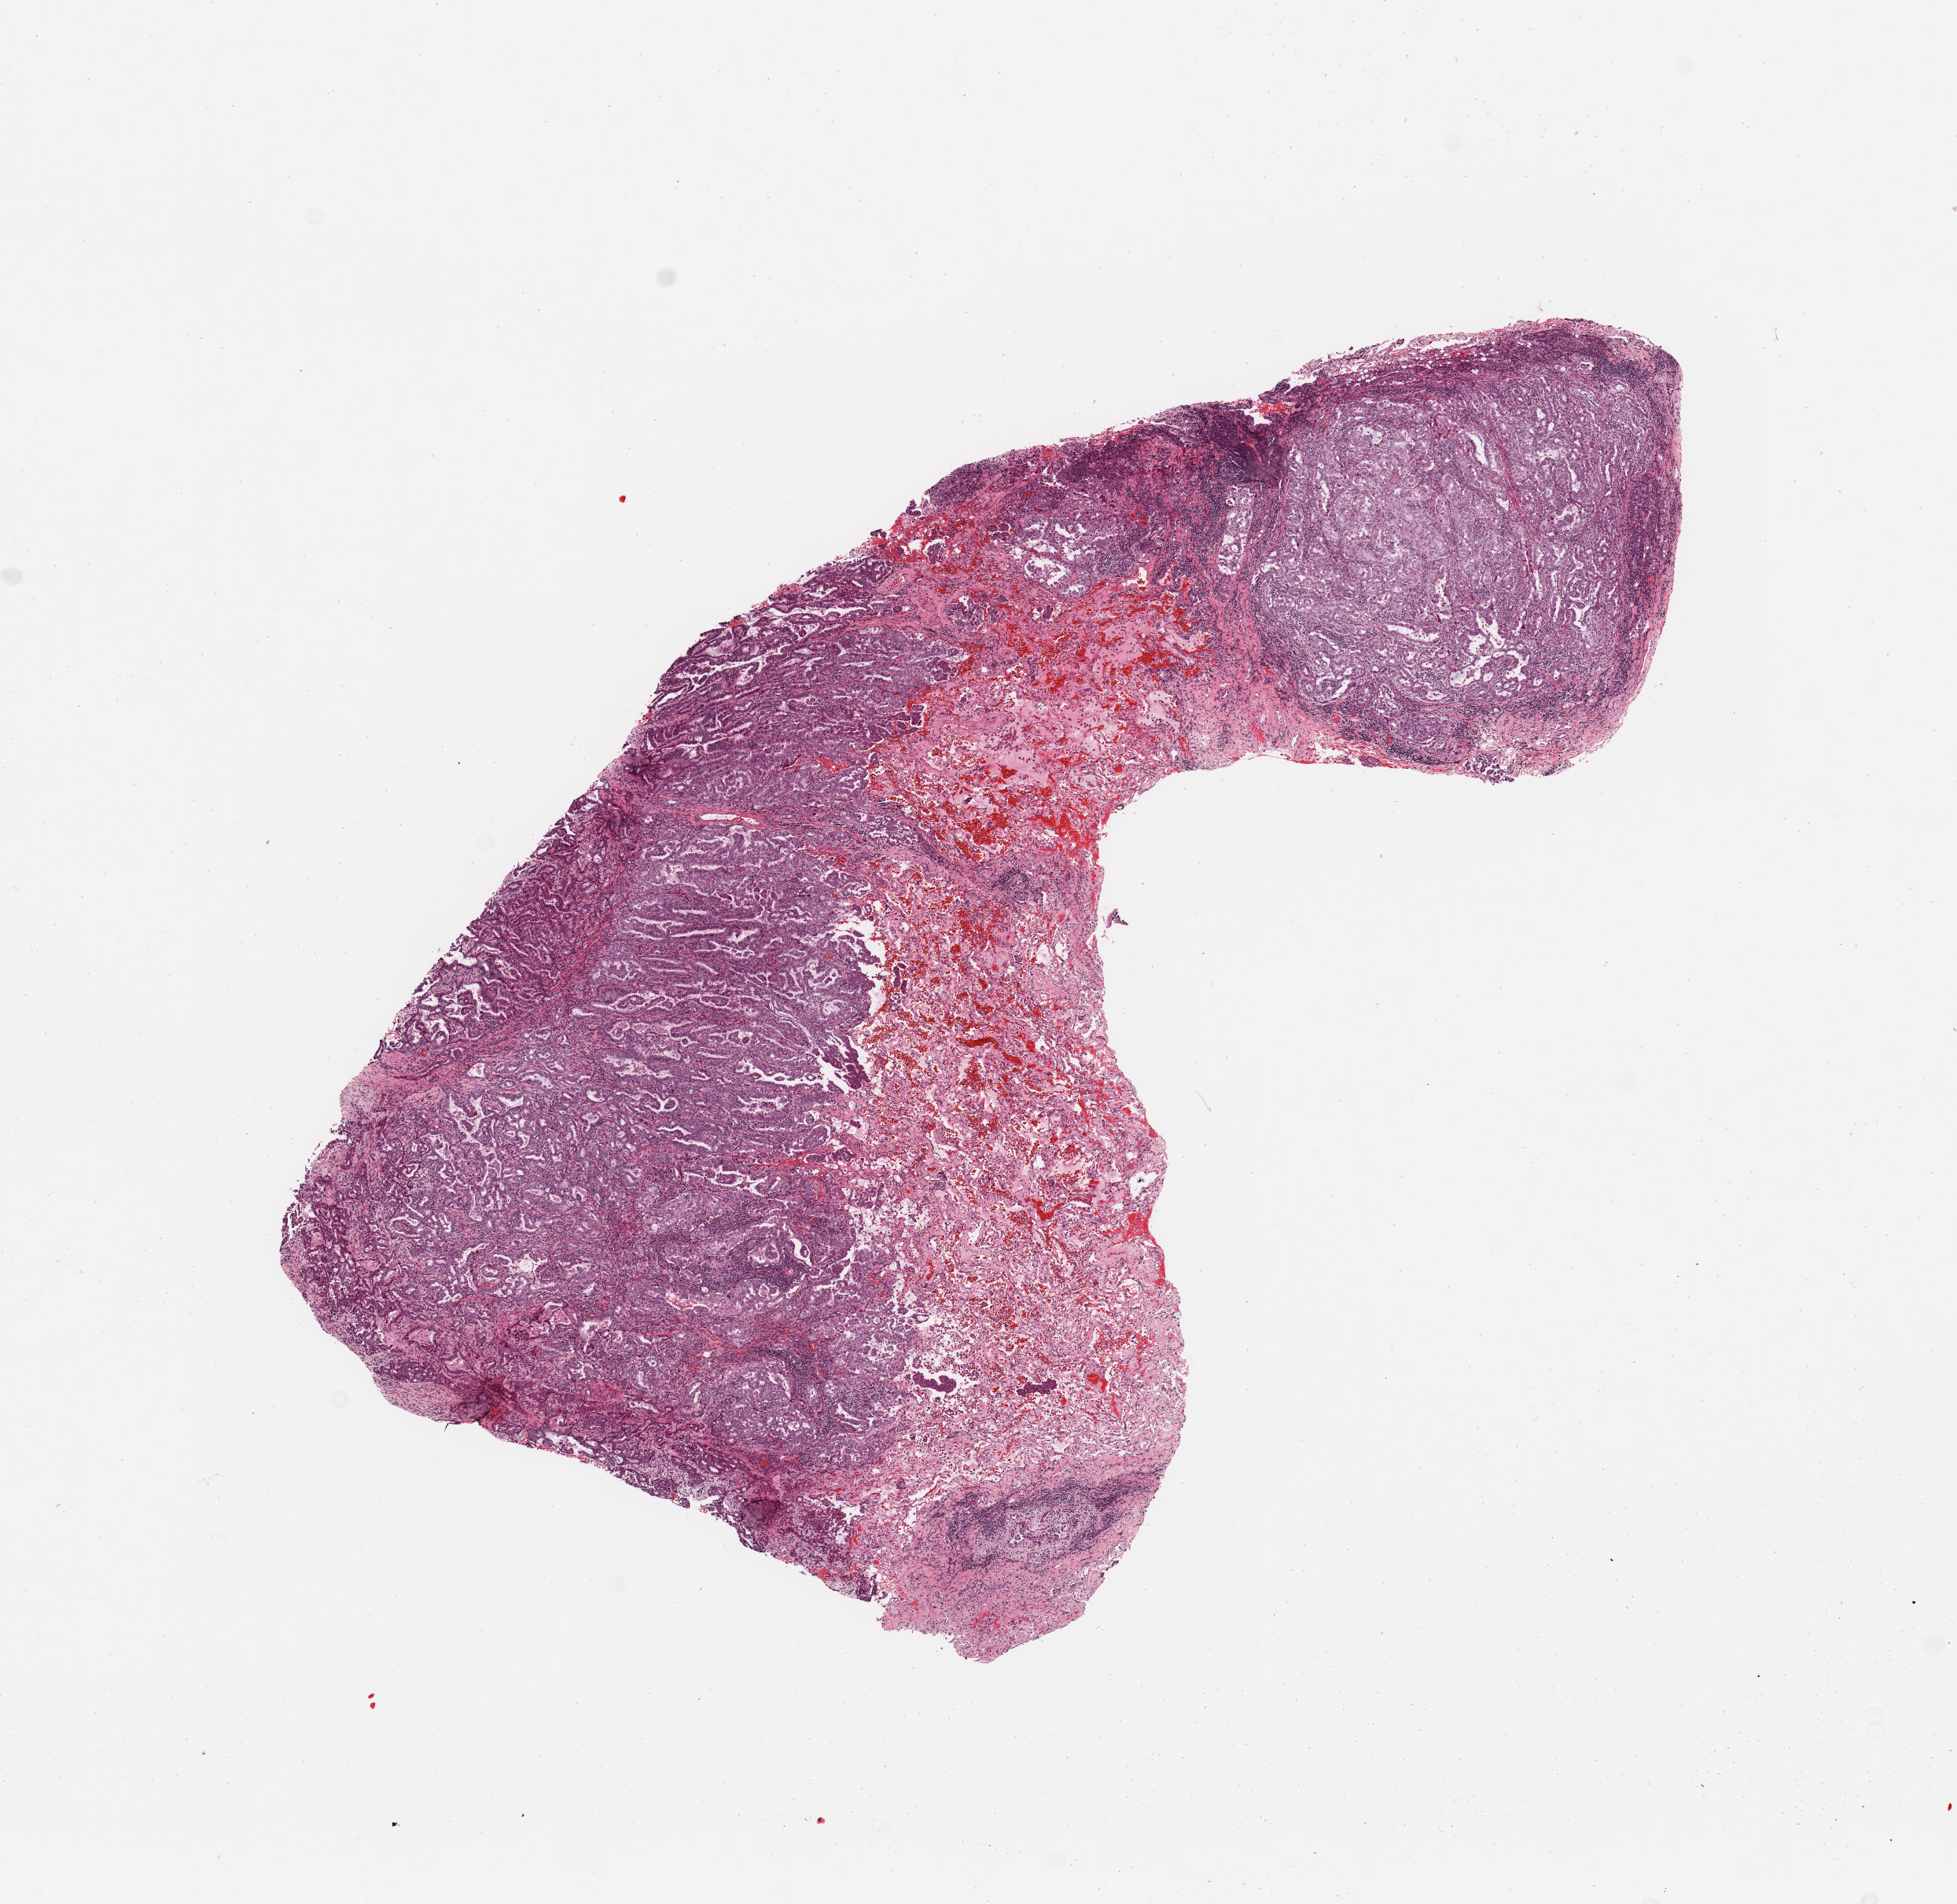
Hematoxylin and eosin (H&E) stained whole-slide image, a low-resolution overview of the entire scanned area, about 9.8 x 9.6 mm. Lung, tumour tissue. Female, 61 y/o. Histologic grade: G2 (moderately differentiated).
Histologic diagnosis: Adenocarcinoma, NOS. Primary tumour site (as recorded): right upper lobe. AJCC pathologic stage: IIIA.